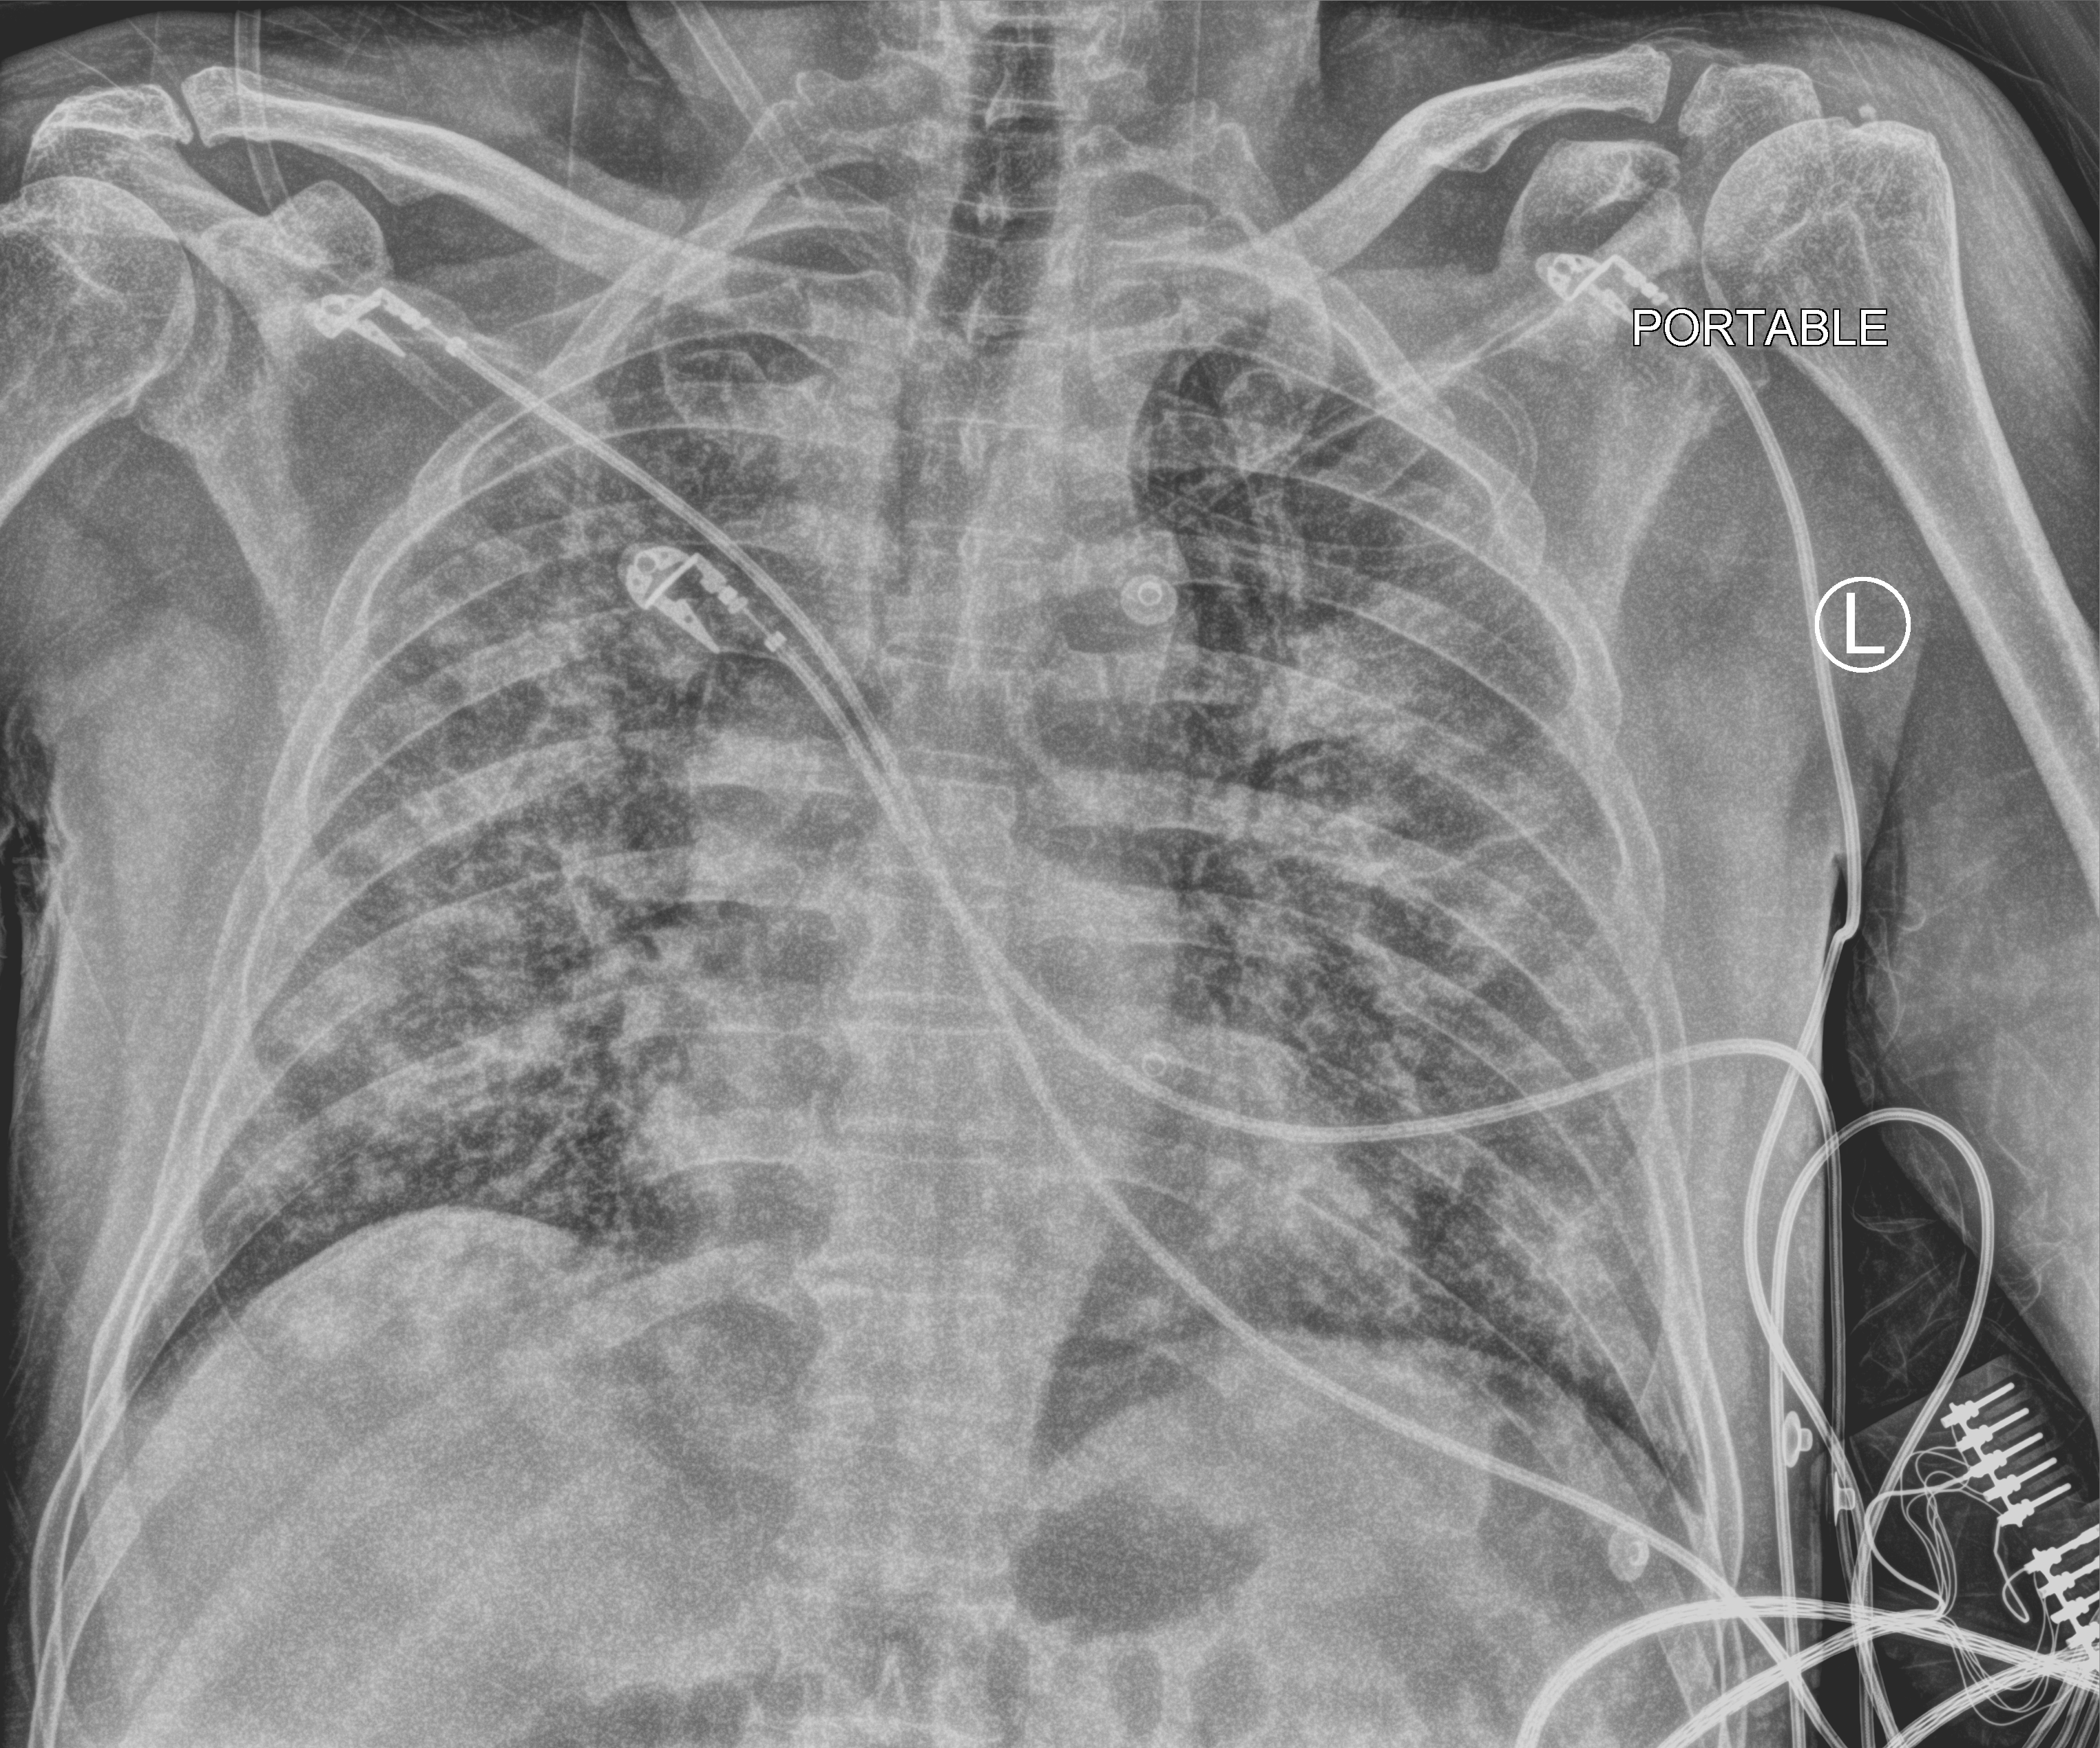
Portable chest radiograph; anteroposterior (AP) projection. Patient hospitalised with COVID-19; male, aged 60–74 years.
From the hospital-stay record, not from the radiograph (when in the stay this image was taken is not recorded):
- mechanically ventilated during this hospital stay: yes
- admitted to intensive care during this hospital stay: yes